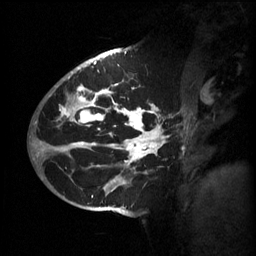
Breast MRI (dynamic contrast-enhanced), one sagittal slice; slice 36 of 60 in the series (ordered by position); 3 images stored at this slice position (order not interpretable as contrast timing); 1.5 T; TE 4.2 ms, TR 11 ms; 2 mm slice thickness; 256 × 256 image matrix, field of view 220 × 220 mm. Patient: female, 51 years.
Outlined on this slice (semi-automatic segmentation, software-assisted and operator-edited):
- analysis volume of interest (the breast-tissue region the enhancement analysis was run in; not a lesion): bounding box <63,80,184,201> (left, top, right, bottom; pixels)
- tumour enhancement mask (voxels above the 70 % enhancement threshold inside the analysis volume of interest): <63,84,167,197>